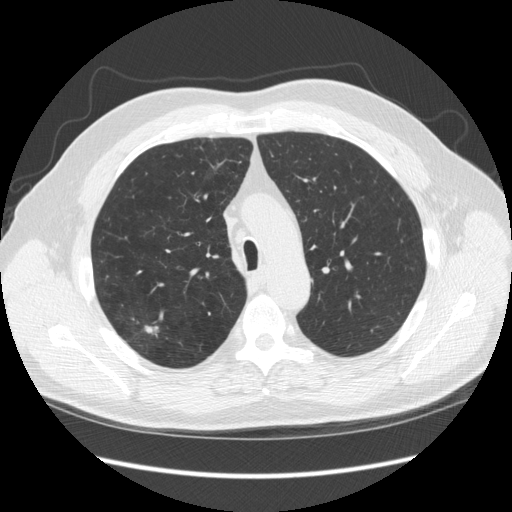
Axial slice from a low-dose chest CT screening exam. Third screening round (two years after baseline). Lung window (W 1500 / L -600 HU). Standard (soft-tissue) reconstruction kernel (STANDARD). Slice 69 of 248 in the series. Male, age 64 years at enrolment. Former smoker at enrolment.
Lesion marked by an expert reader, bounding box <117,314,171,358> (left, top, right, bottom; pixels). The screening reader recorded 4 non-calcified nodules or masses ≥4 mm on this exam; which of them this box marks is not recorded. Official screen result: positive, other. Participant outcome: lung cancer diagnosed 15 days after this screen — adenocarcinoma, NOS, right upper lobe, moderately differentiated (G2), stage IA (AJCC 6th edition), 14 mm at pathology.